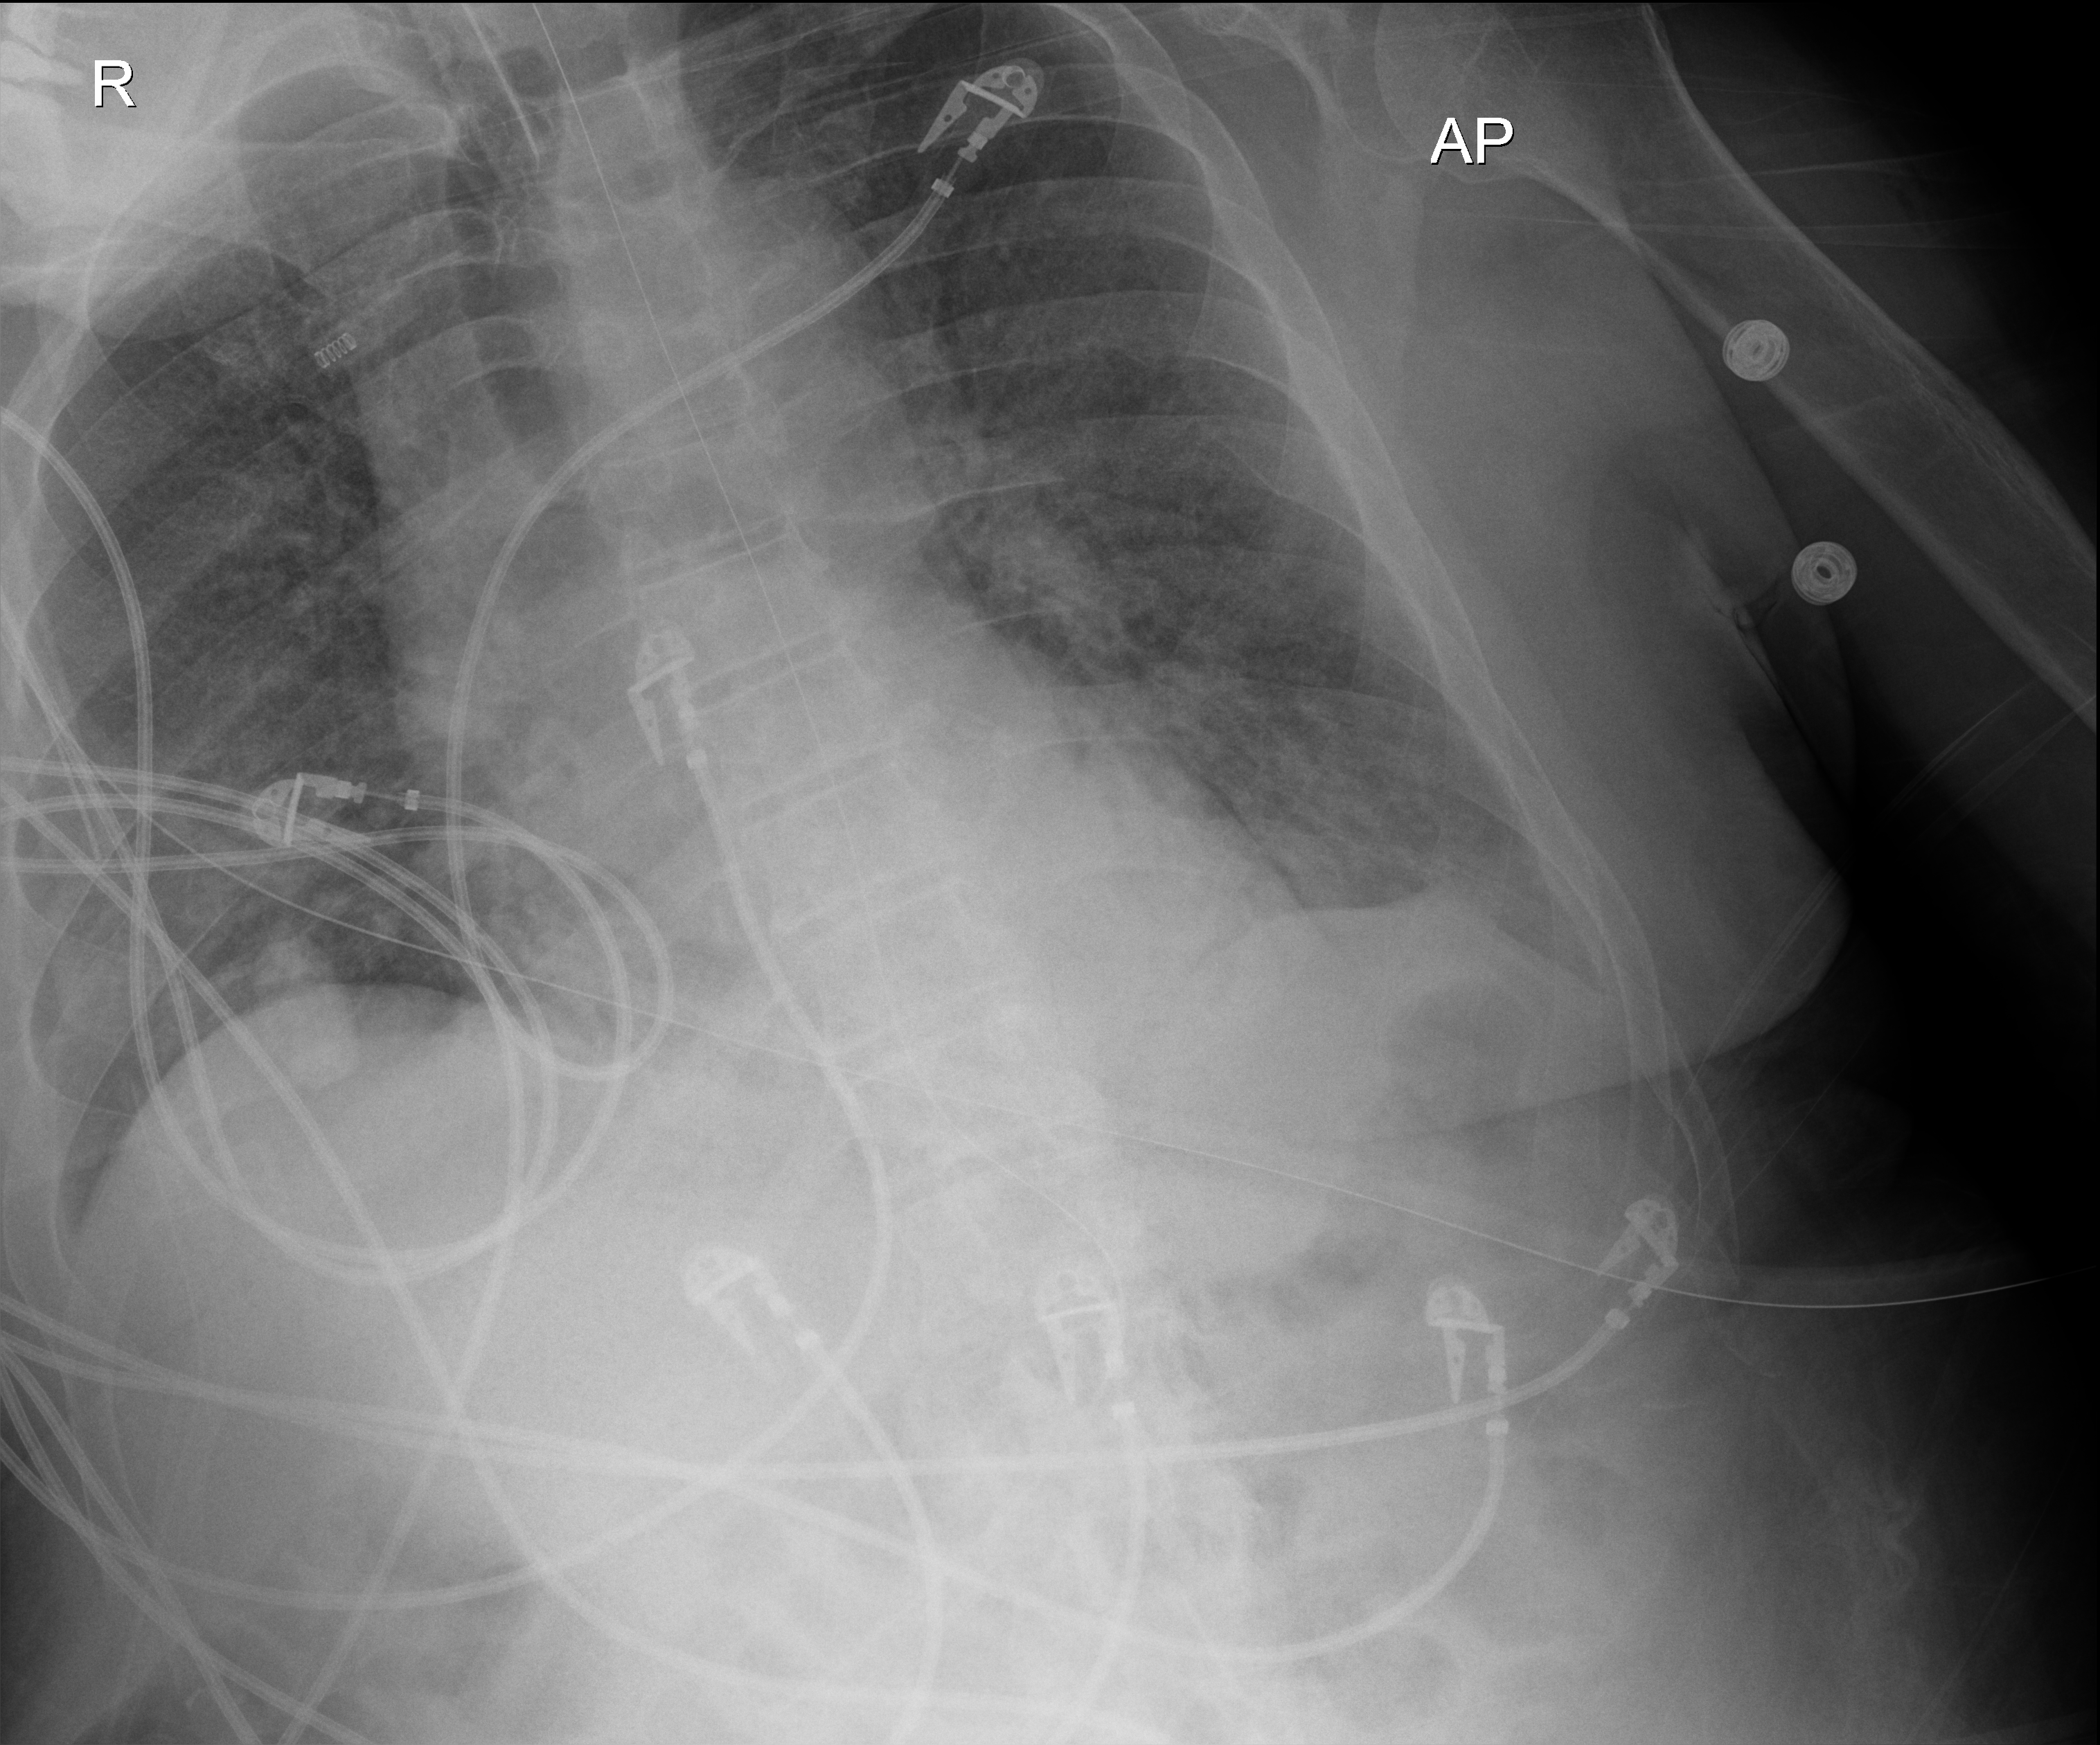
Portable chest radiograph. Male patient hospitalised with COVID-19, age 60–74 years.
From the hospital-stay record, not from the radiograph (when in the stay this image was taken is not recorded):
- COPD (admission record): no